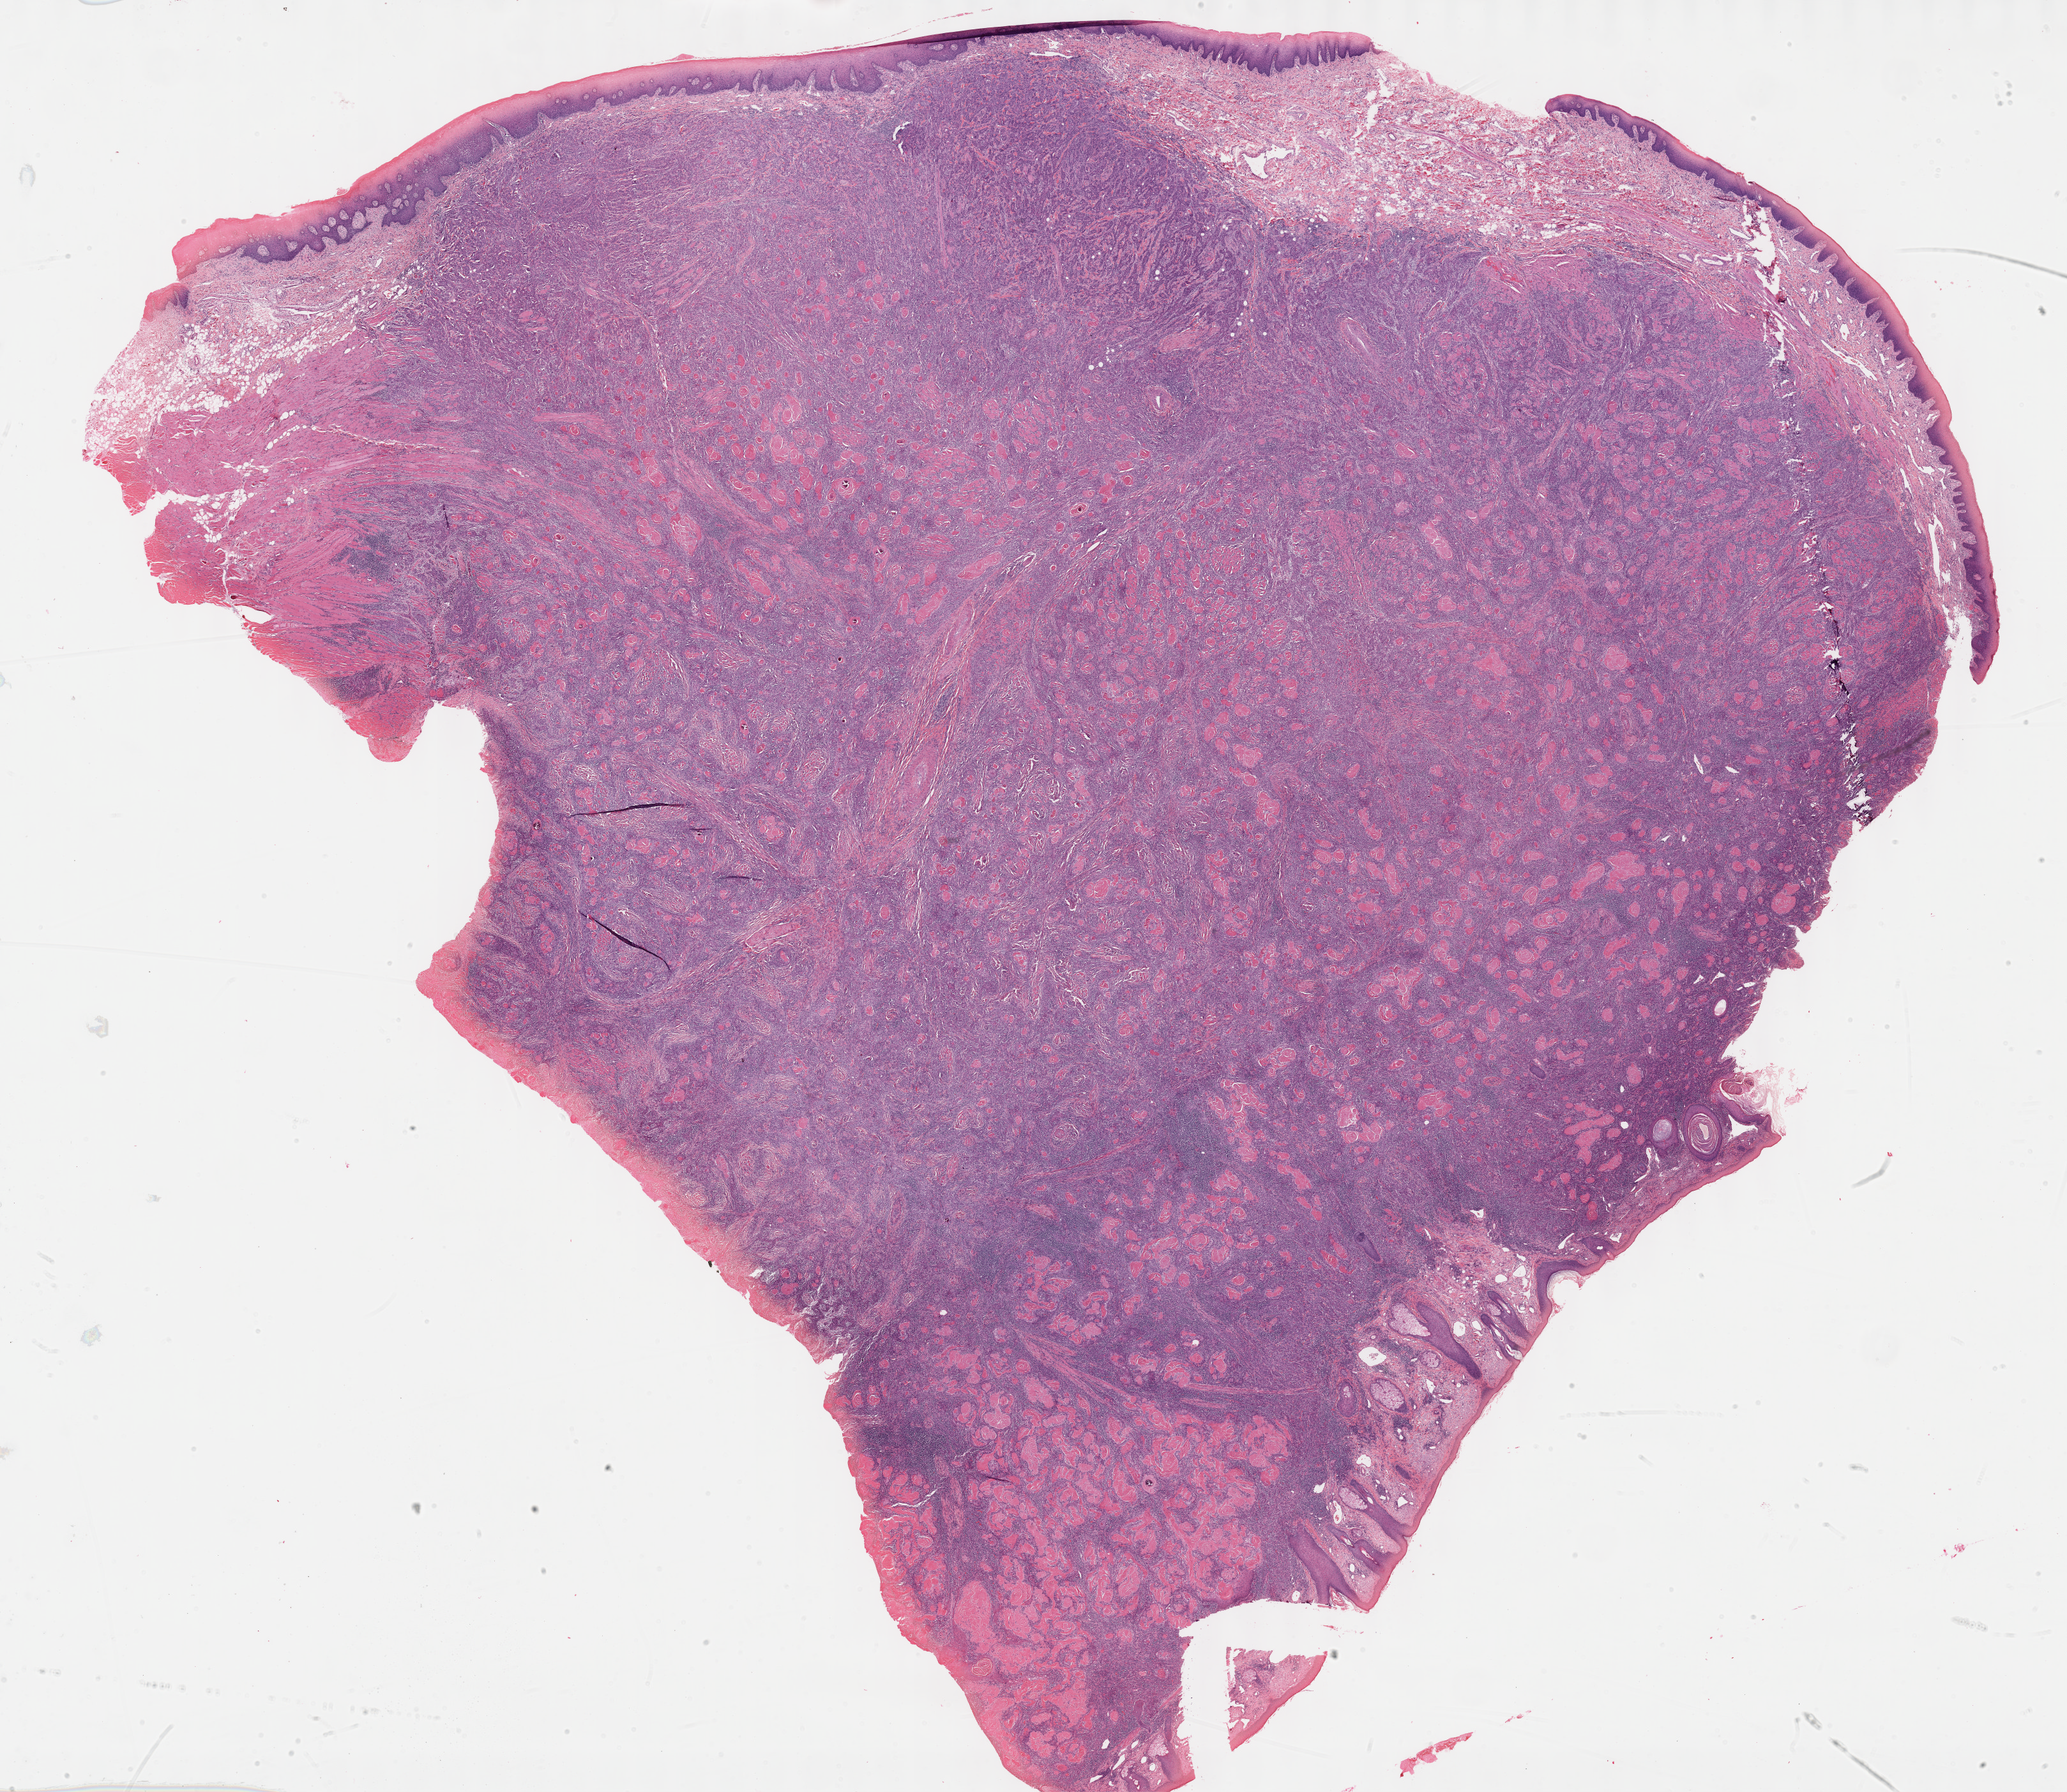
Digitized H&E tissue section (whole slide) — shown as a low-resolution overview of the whole scanned area (about 26.2 x 22.7 mm); formalin-fixed paraffin-embedded (FFPE) diagnostic section; head and neck, primary tumour sample. Male patient; age at initial diagnosis 42 years. Histologic grade: G2 (moderately differentiated).
TNM: T4a N2a M0. Lymph nodes positive (case pathology): 2 of 34 examined. AJCC pathologic stage: IVA (5th edition). Histologic diagnosis: Squamous cell carcinoma, keratinizing, NOS.